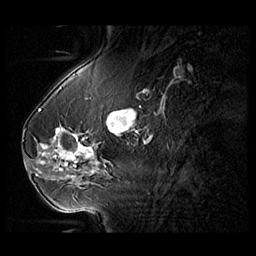
Breast MRI (dynamic contrast-enhanced), one sagittal slice. Position 37 of 104 along the scan axis. 3 images stored at this slice position (order not interpretable as contrast timing). 1.5 T. TE 1.3 ms, TR 5.5 ms. 256 × 256 image matrix, field of view 220 × 220 mm. Female patient, age 54 years. From the clinical record (not read from this slice): setting: breast cancer imaged before/during neoadjuvant chemotherapy; receptor status: HR-positive, HER2-negative.
Structures marked on this image (semi-automatic segmentation, software-assisted and operator-edited):
- analysis volume of interest (the breast-tissue region the enhancement analysis was run in; not a lesion): bounding box <28,127,104,182> (left, top, right, bottom; pixels)
- tumour enhancement mask (voxels above the 140 % enhancement threshold inside the analysis volume of interest): <41,129,94,170>